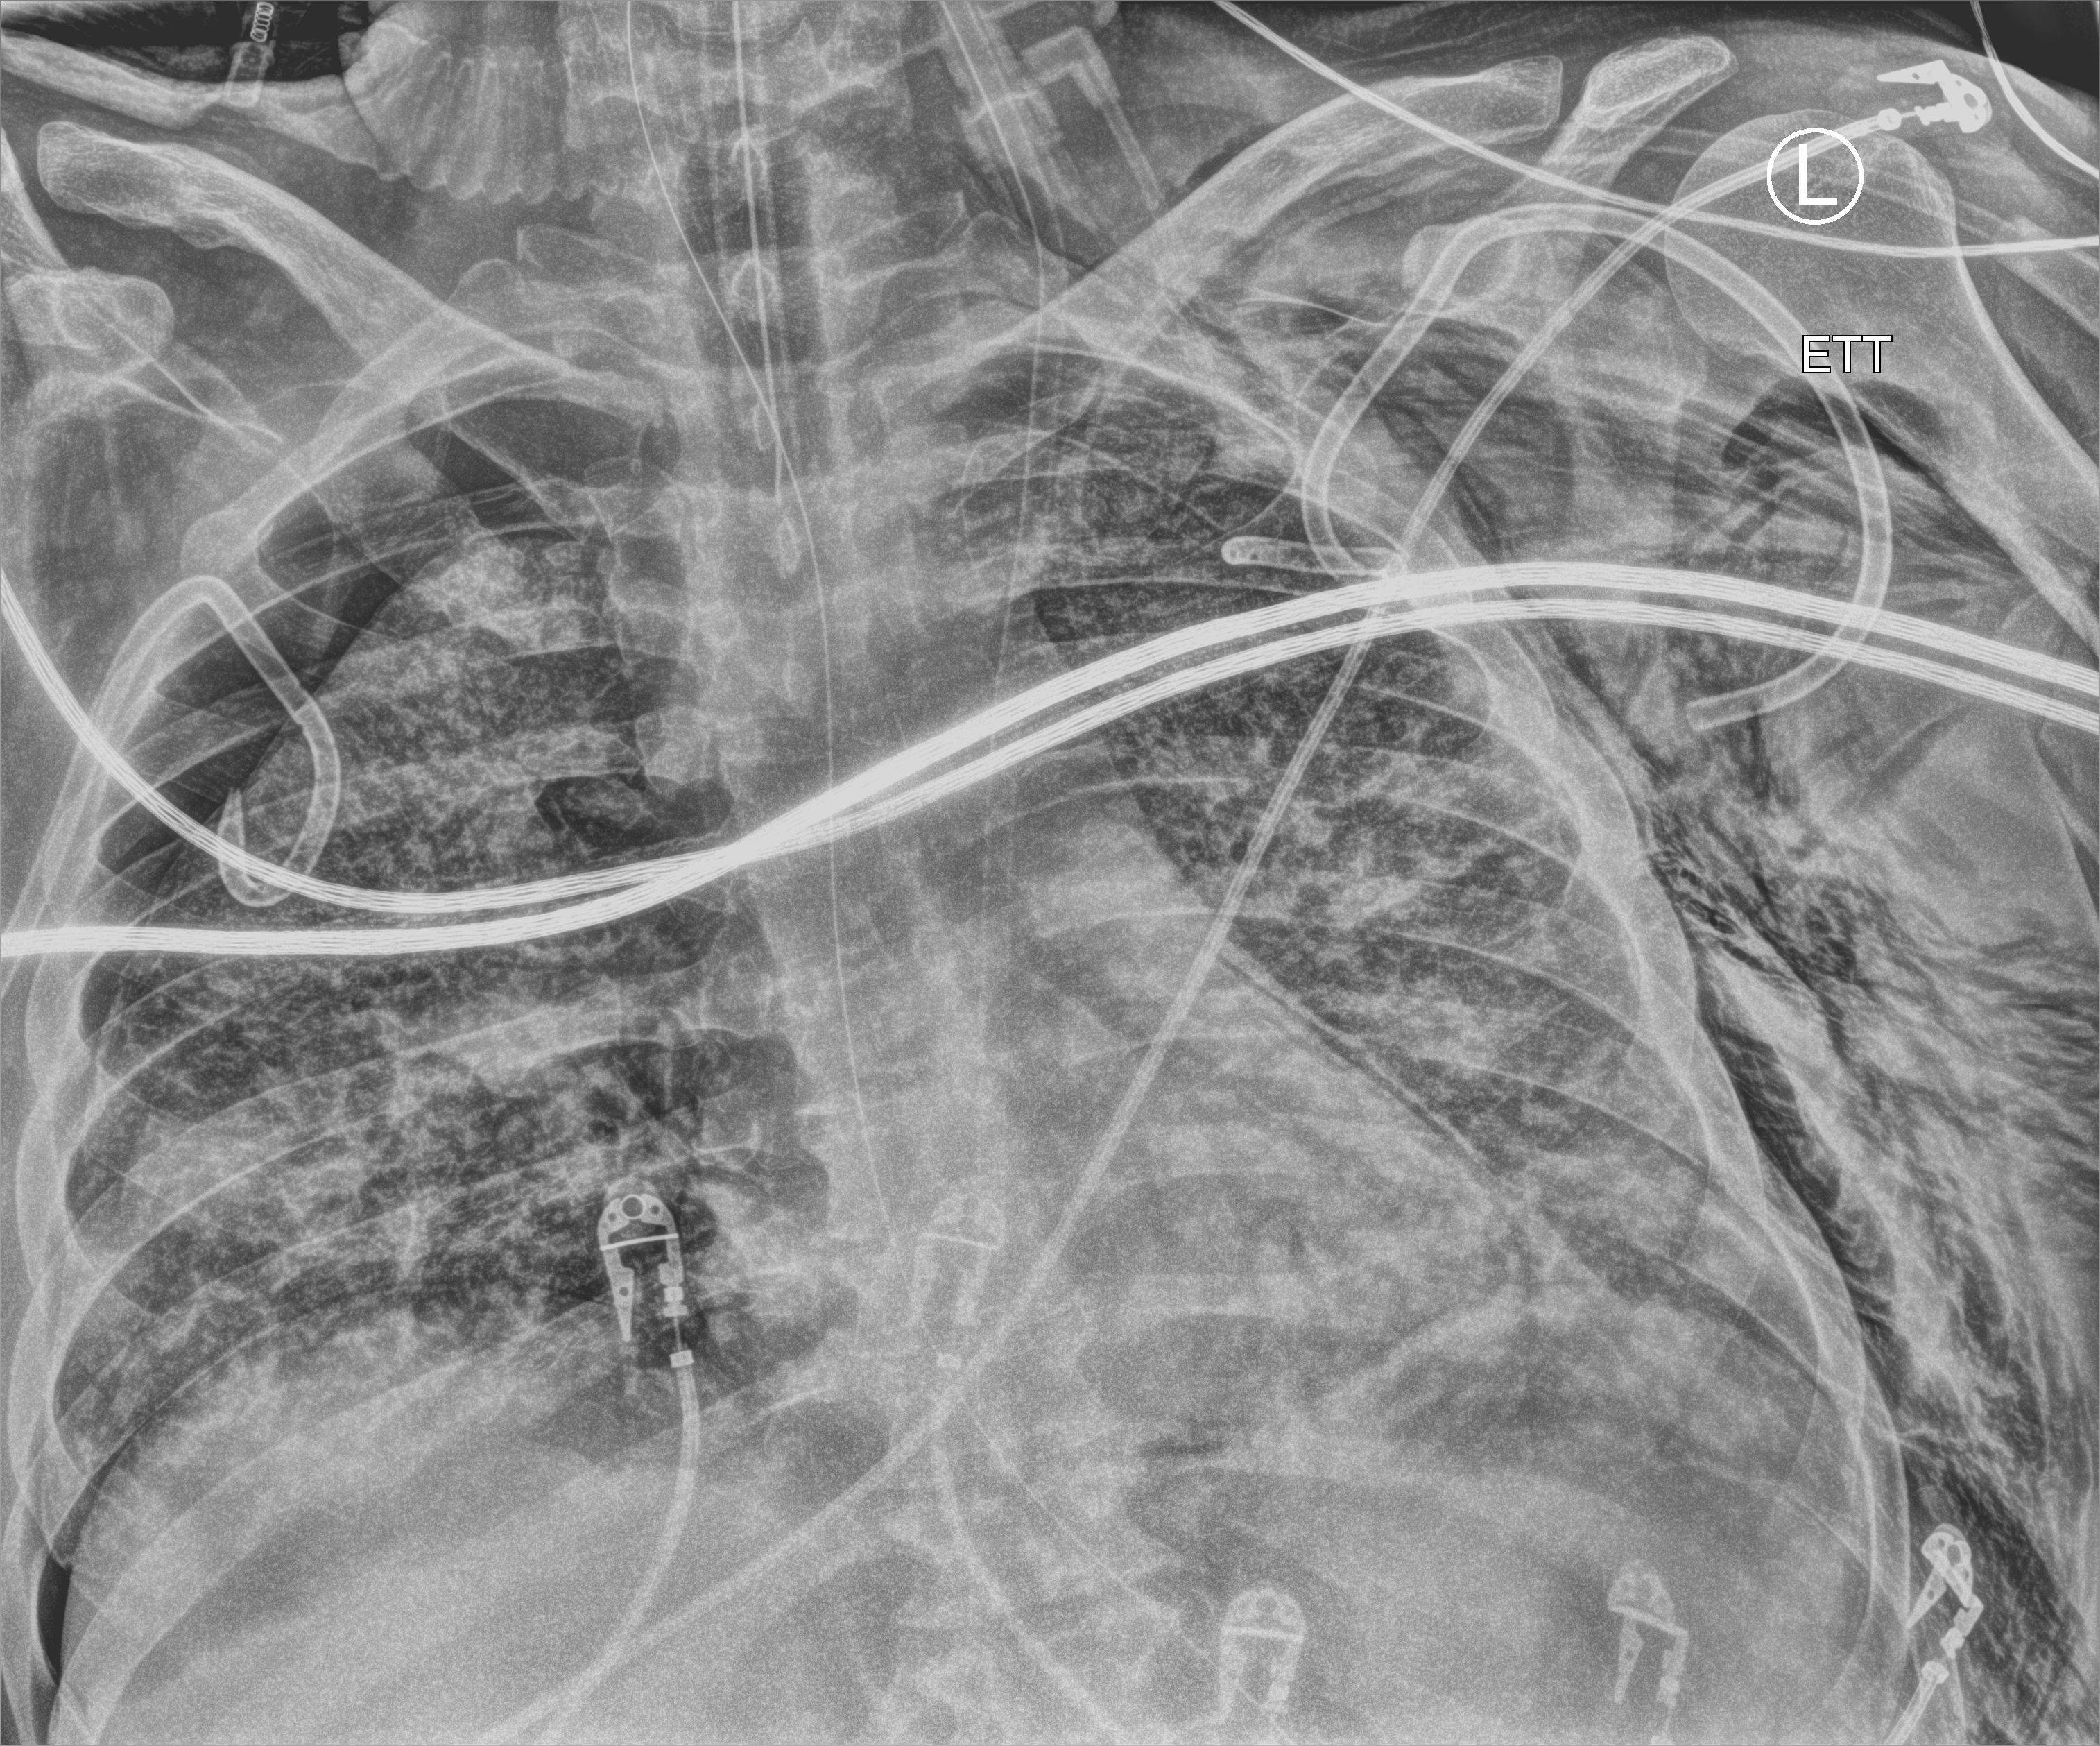
Chest X-ray (portable), anteroposterior (AP) projection. Patient hospitalised with COVID-19, aged 18–59 years.
From the hospital-stay record, not from the radiograph (when in the stay this image was taken is not recorded): admitted to intensive care during this hospital stay: yes; mechanically ventilated during this hospital stay: yes.